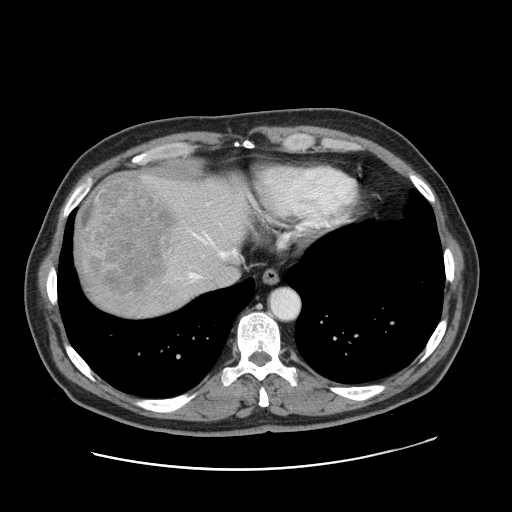
Contrast-enhanced abdominal CT, one axial slice. Slice 141 of 178 in the series (ordered by position). 120 kVp. Intravenous contrast given. Soft-tissue window (W 400 / L 40 HU). 2.5 mm slice thickness. 512 × 512 image matrix, field of view 403 × 403 mm. Male patient, age 63 years. Case-level facts recorded for this patient, not image findings: diagnosis: colorectal cancer liver metastases, imaged before liver resection; multiple liver metastases: yes; largest metastasis: 8 cm; chemotherapy before resection: no.
Annotated regions visible in this slice (outlined manually by an expert reader):
- hepatic veins: box from (x=190, y=233) to (x=237, y=278) px
- liver: (x=74, y=171)–(x=250, y=320)
- planned liver remnant (the part of the liver to remain after resection): (x=178, y=175)–(x=248, y=279)
- liver metastasis: (x=77, y=175)–(x=174, y=296)